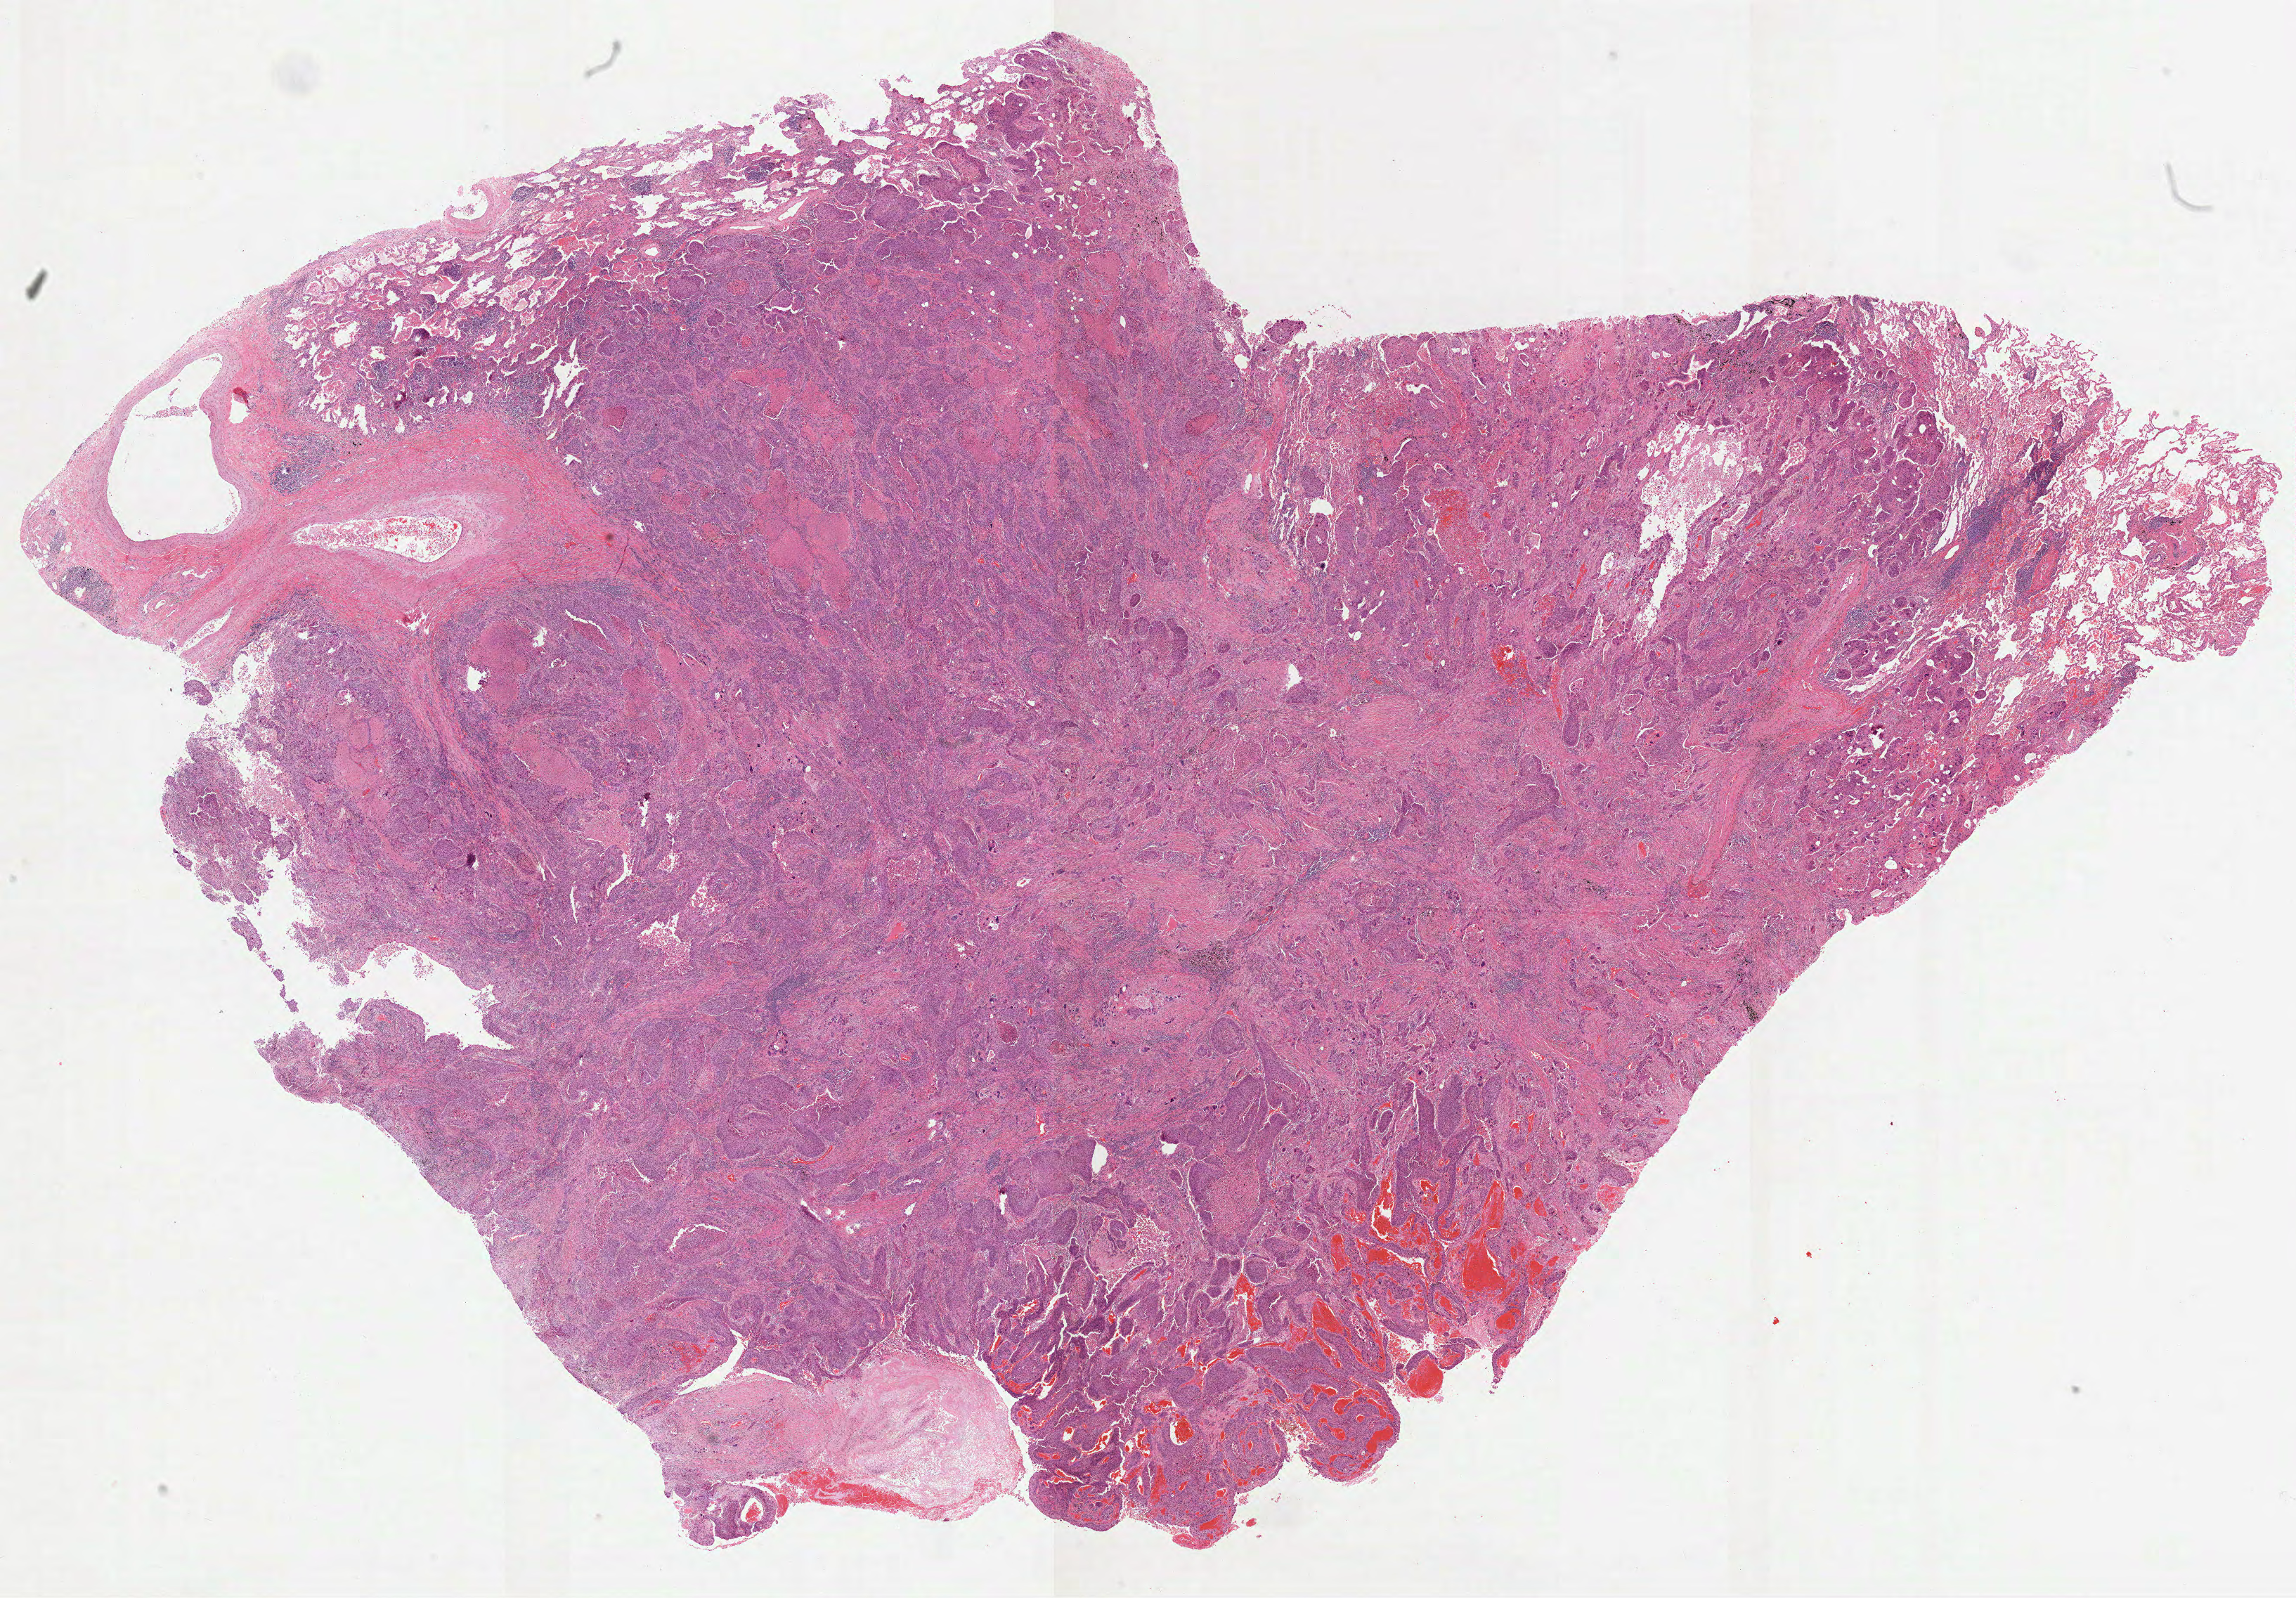
Digitized H&E-stained tissue section (whole slide) — whole scanned area (about 26.3 x 18.3 mm, slide scanned at 40x) shown as a low-resolution overview, formalin-fixed paraffin-embedded (FFPE) diagnostic section, sample: primary tumour, lung. Patient: male, age at initial diagnosis 72 years.
Diagnosis: Squamous cell carcinoma, NOS (lower lobe, lung). AJCC pathologic stage: IIIA (7th edition). Laterality: right.